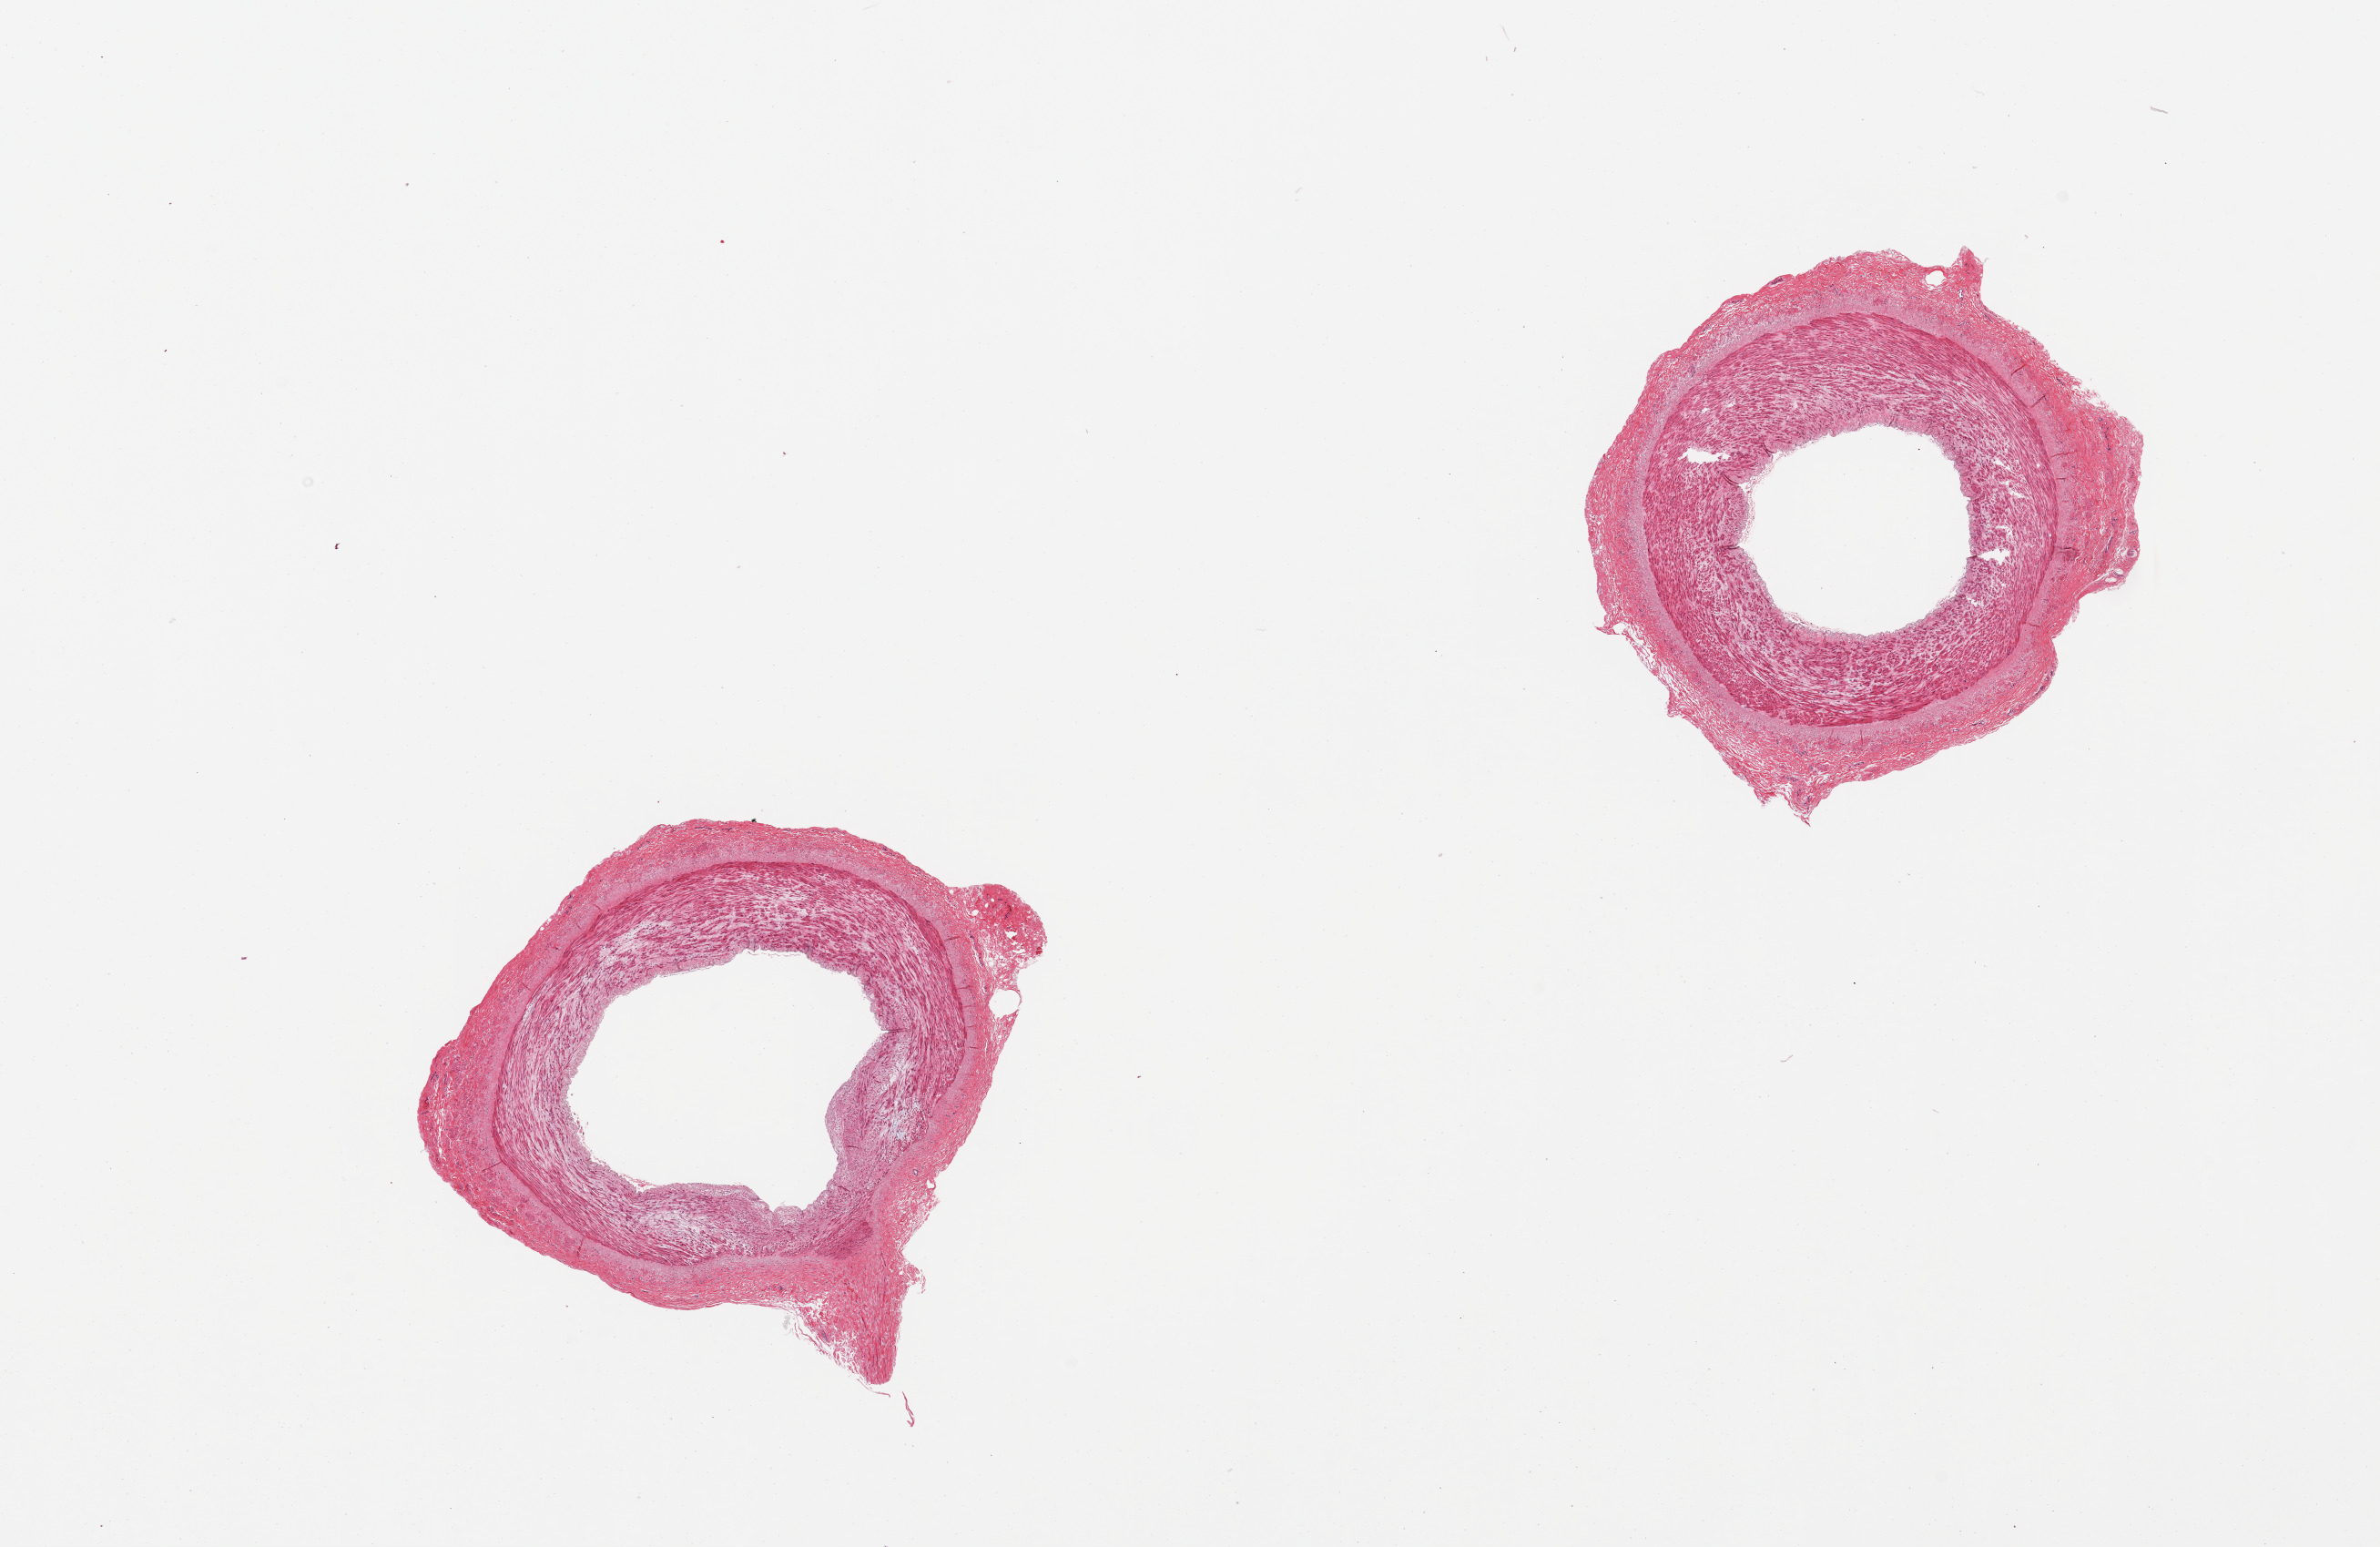
Whole-slide image, H&E stain, brightfield, shown as a low-resolution overview of the whole scanned area (about 20.7 x 13.4 mm, slide scanned at 20x). PAXgene-fixed, paraffin-embedded tissue. Target tissue: tibial artery. Tissue donor sample. Donor: female.
* reviewer comment on this tissue sample: 2 pieces, well trimmed